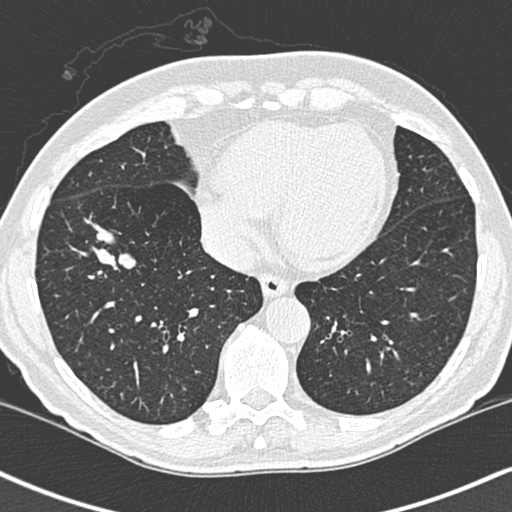
Low-dose screening chest CT, one axial slice; position 89 of 248 along the scan axis; lung window (W 1500 / L -600 HU); 512 × 512 image matrix, field of view 323 × 323 mm.
Annotated regions visible in this slice (manually delineated by an expert):
- lesion 1 (tumor, lower lobe of right lung): bounding box (x1, y1, x2, y2) in pixels: (84, 177, 136, 232)